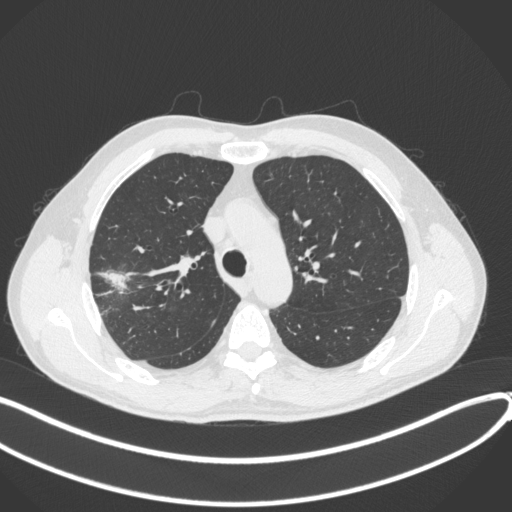
Chest CT, one axial slice; slice 302 of 381 in the series (ordered by position); reconstruction kernel B31f; 120 kVp; lung window (W 1500 / L -600 HU); 1 mm slice thickness; 512 × 512 image matrix, field of view 400 × 400 mm. Male patient, age 62 years. From the clinical record (not read from this slice): clinical TNM (as recorded): T1c N0 M0.
Structures marked on this image (rectangle marked by the reading radiologist):
- lung tumour (recorded histology: adenocarcinoma): bounding box [x1, y1, x2, y2] px = [97, 259, 133, 294]